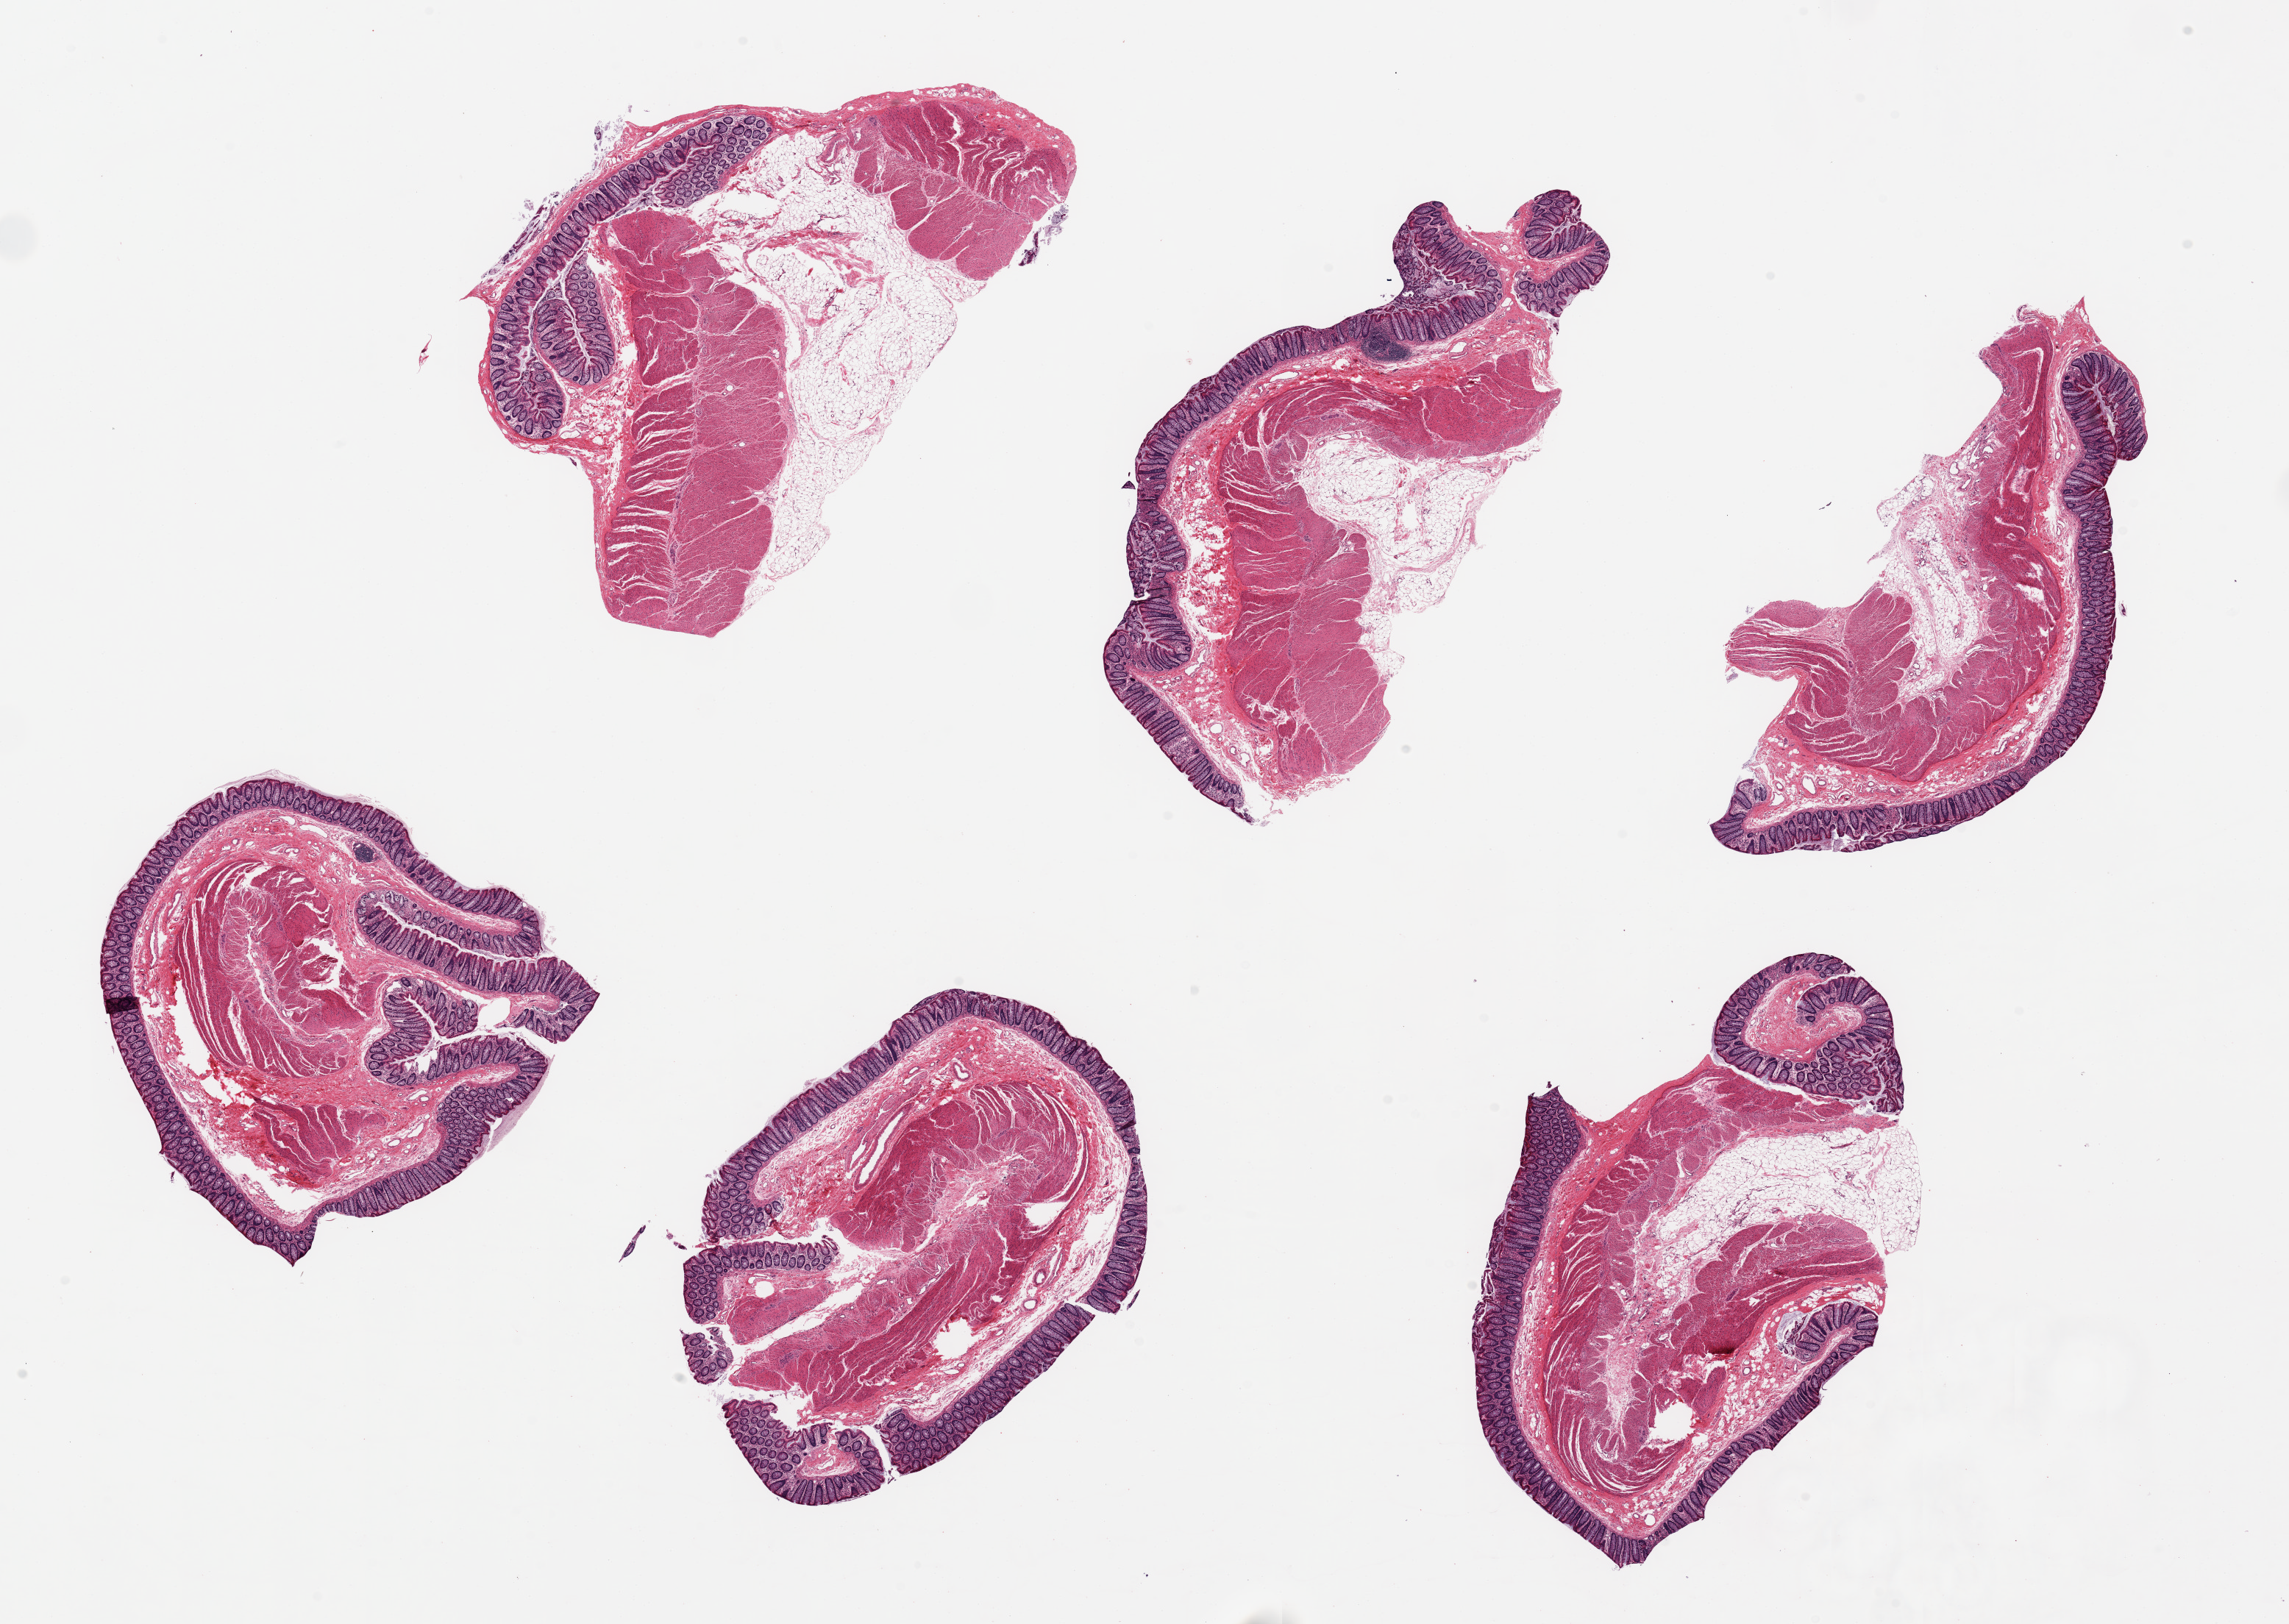
Whole-slide image, hematoxylin and eosin (H&E) stain, brightfield, low-resolution overview of the scanned area, about 24.6 x 17.5 mm (acquisition: 20x scan). PAXgene-fixed, paraffin-embedded tissue. Sampled site (target tissue): transverse colon. Tissue donor sample. Donor: female.
Review note (as recorded): 6 pieces up to 7x4 mm; mucosa ~0.4 mm; very good mucosal preservation in all 6 pieces.